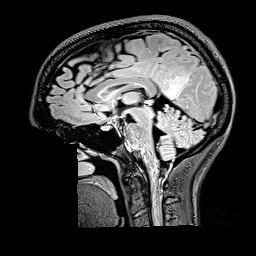
Brain MRI from a brain-tumour surgery series, one sagittal slice. Slice 88 of 176 in the series (ordered by position). T2 FLAIR. 256 × 256 image matrix, field of view 256 × 256 mm. Case-level facts recorded for this patient, not image findings: histopathology: Oligodendroglioma; WHO grade: 2; IDH mutation: yes; tumour location: Right Parietal.
Annotated regions visible in this slice (manually delineated by an expert):
- tumour: bounding box <162,73,190,99> (left, top, right, bottom; pixels)